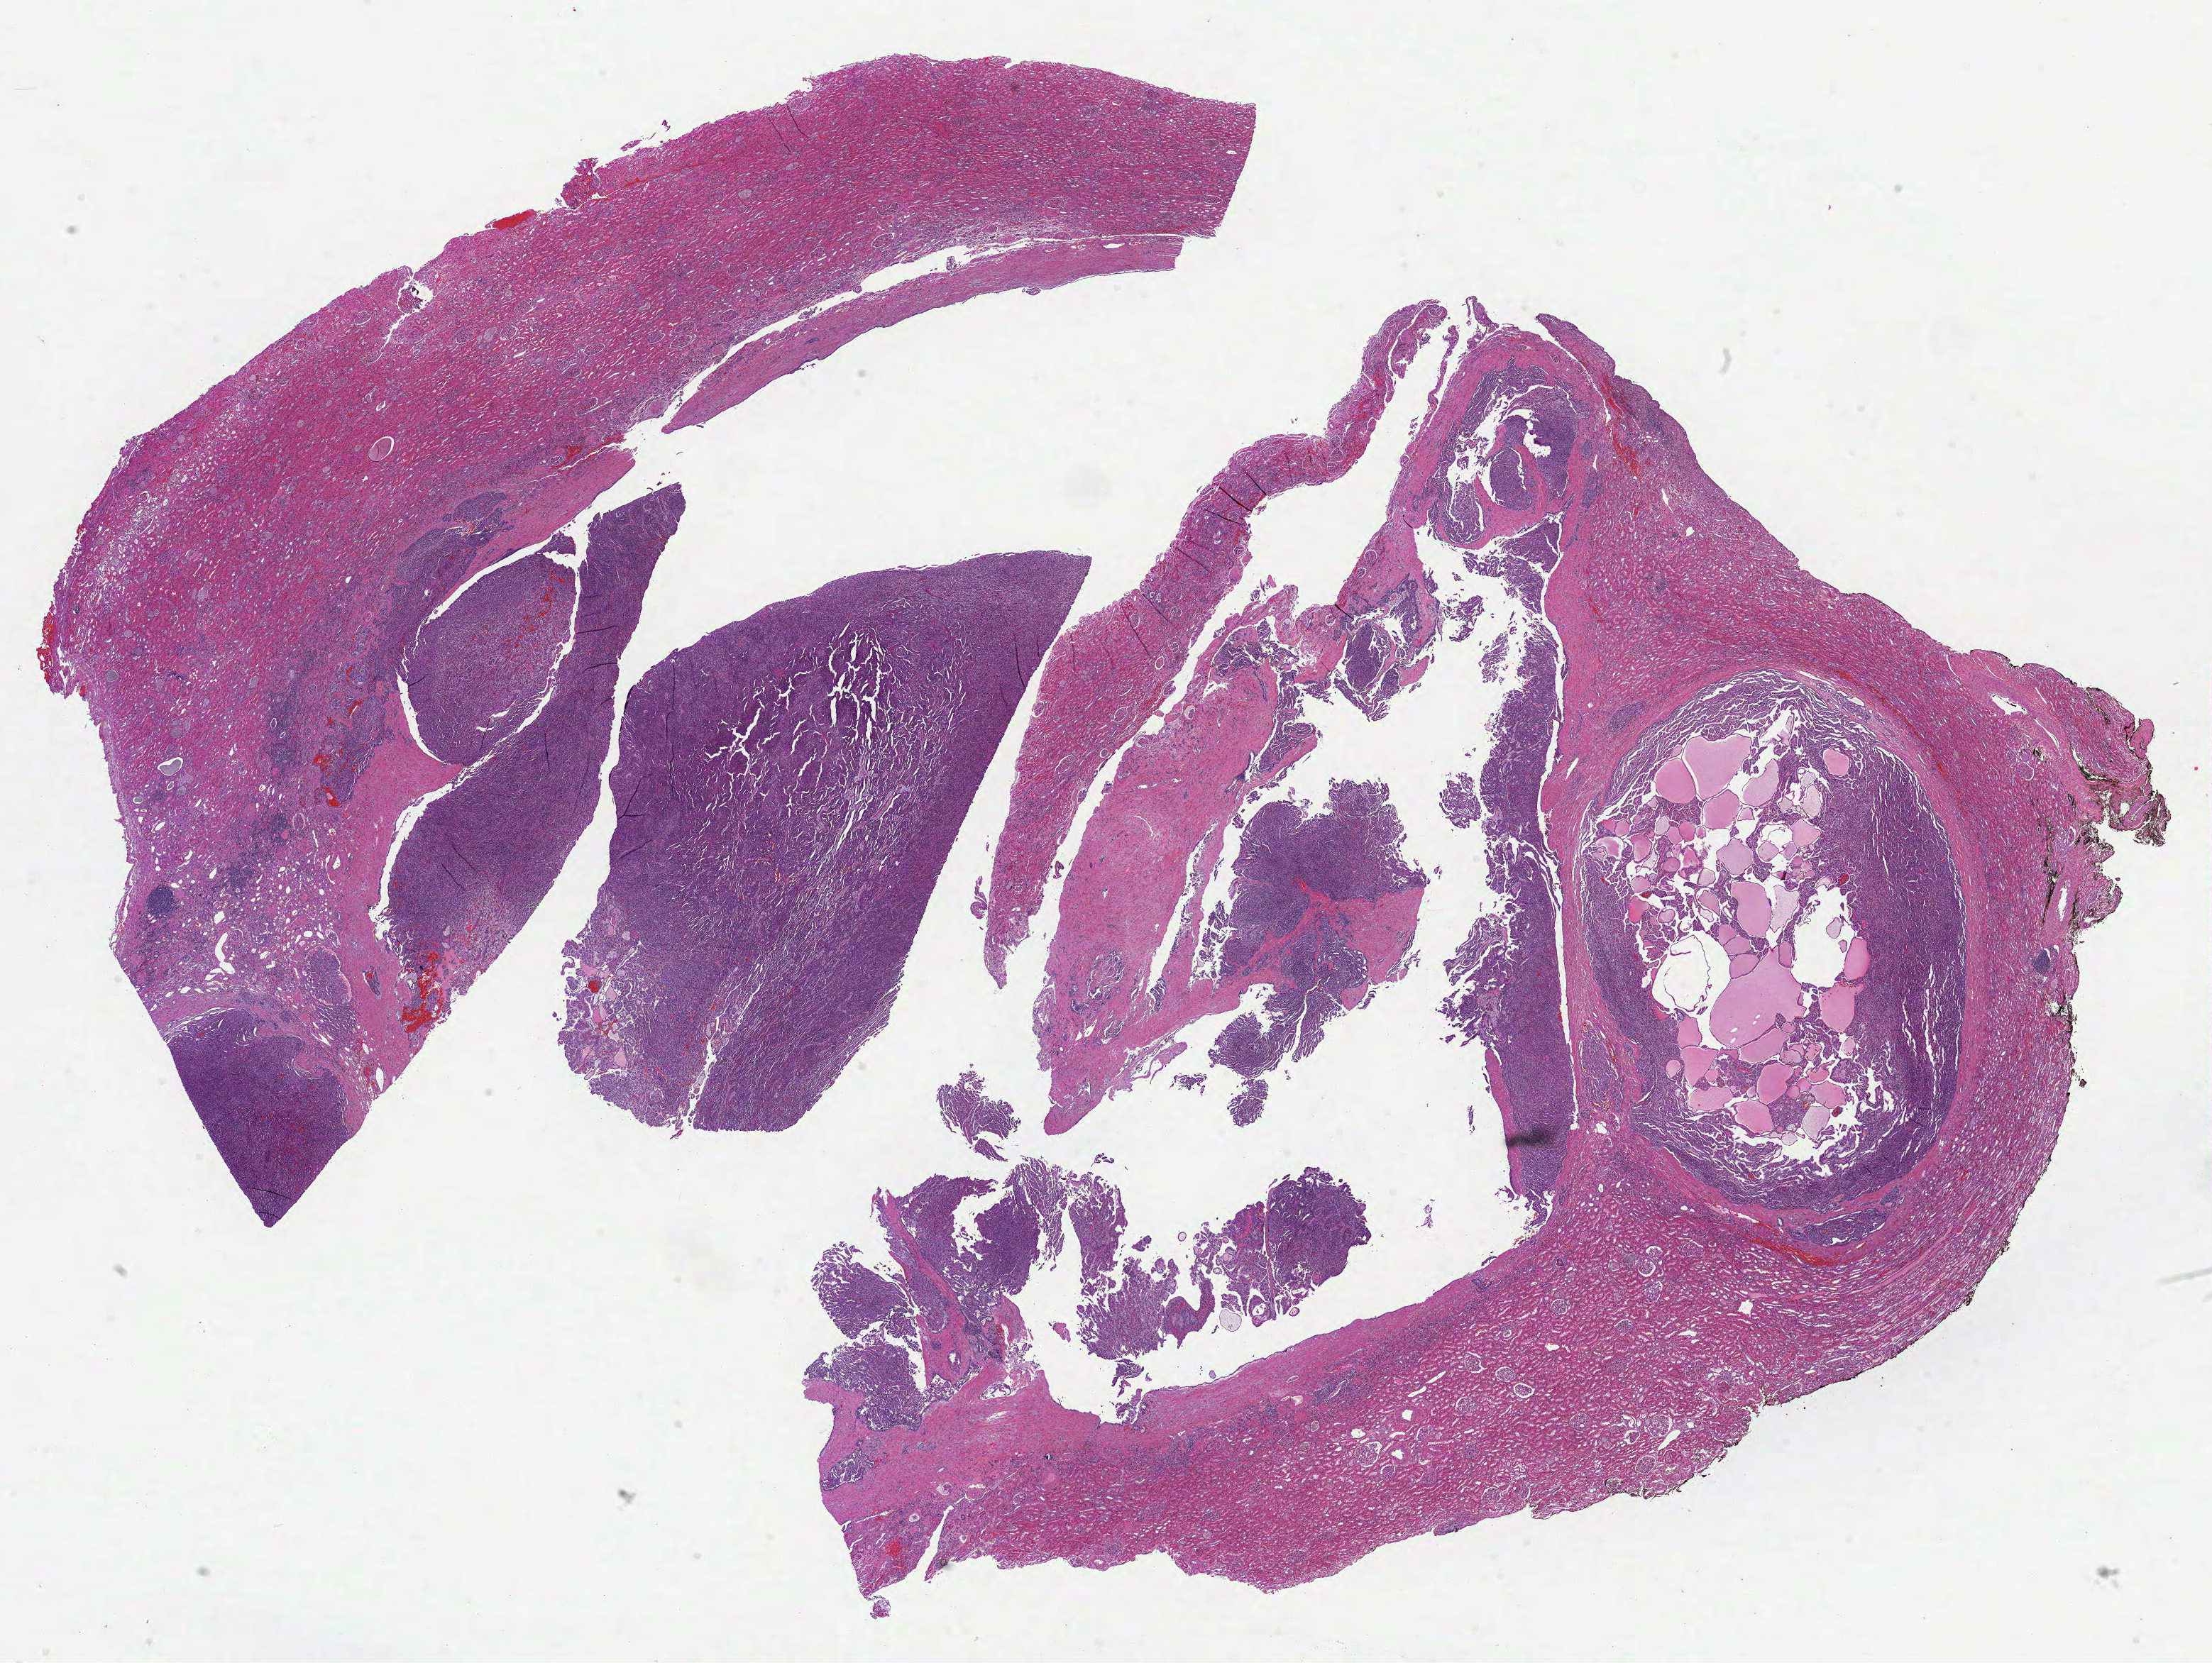
Hematoxylin and eosin (H&E) stained whole-slide image, a low-resolution overview of the entire scanned area, about 25.1 x 18.9 mm; formalin-fixed paraffin-embedded (FFPE) diagnostic section; kidney, primary tumour sample. Male patient; age at initial diagnosis 52 years.
Histologic diagnosis: Papillary adenocarcinoma, NOS.